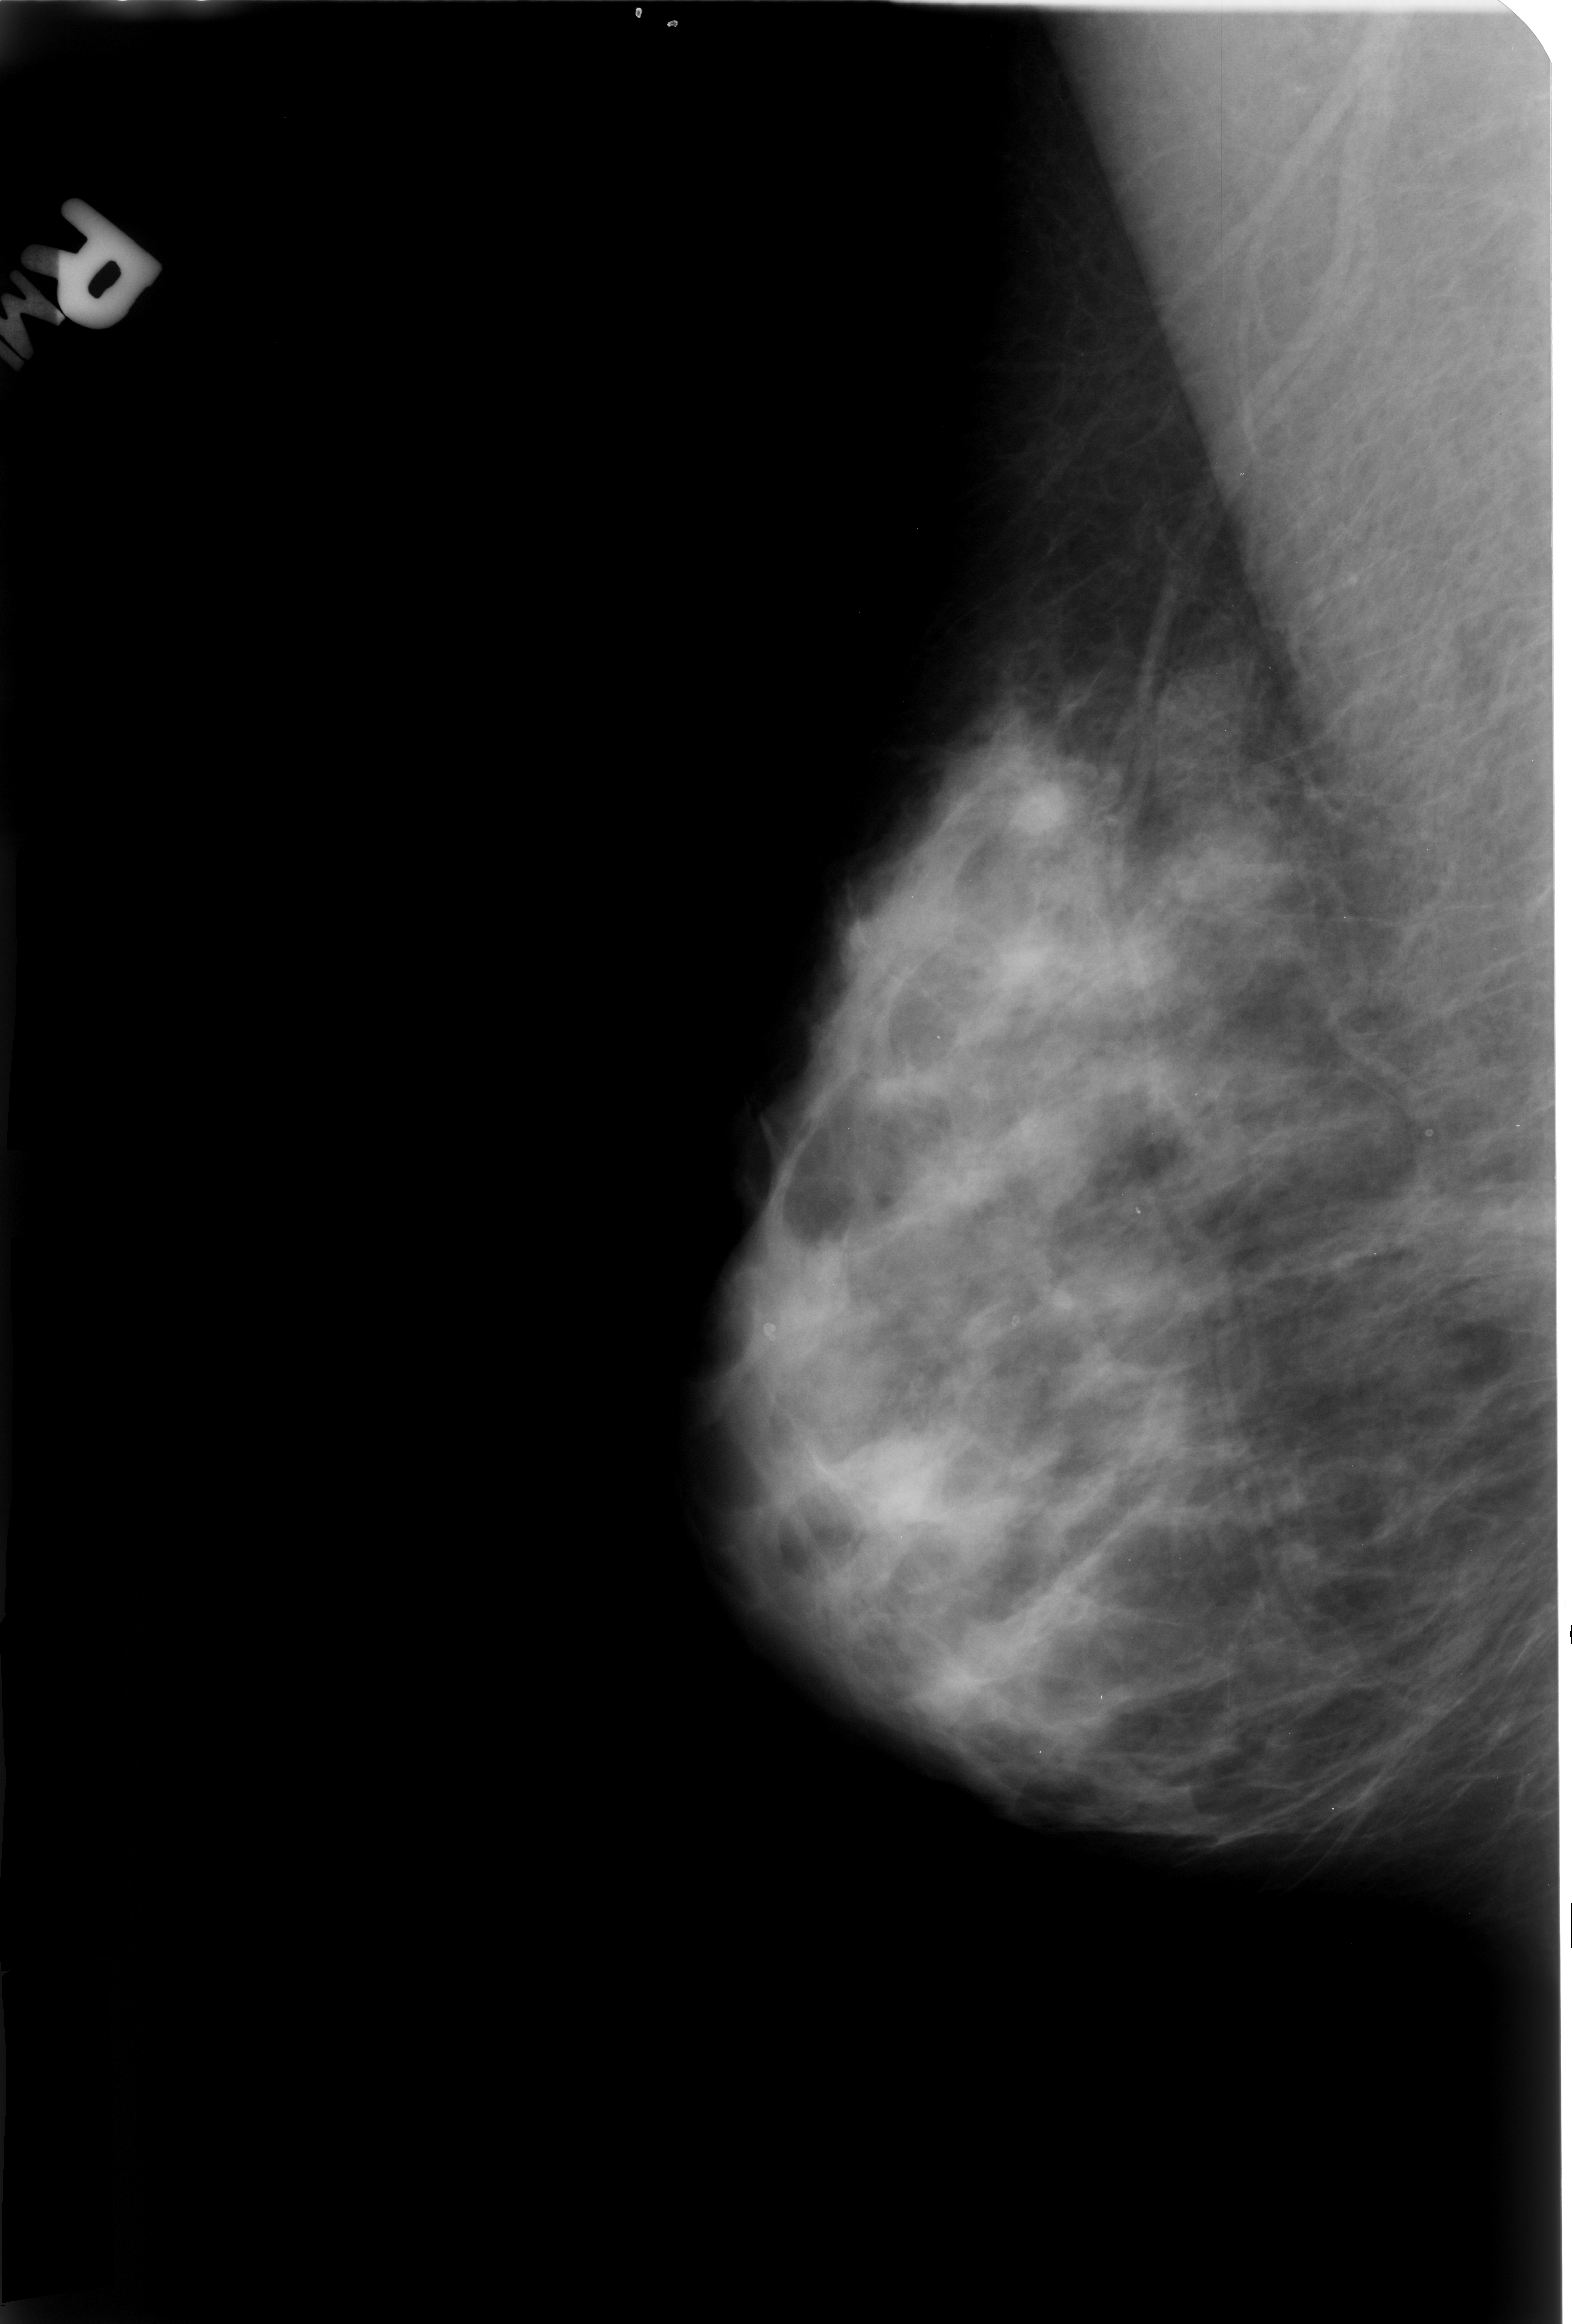
Scanned film-screen mammogram; right breast; MLO view; breast composition: heterogeneously dense (BI-RADS density category 3 of 4); 1572 × 2324 image matrix.
Expert-marked regions of interest on this film, with their recorded descriptors:
- calcifications, morphology lucent center; BI-RADS assessment category 2; subtlety rating 3 on a 1 (subtle) to 5 (obvious) scale; benign; no additional work-up was recommended (outcome (as recorded, no biopsy): benign without callback): bounding box <1119,1200,1157,1234> (left, top, right, bottom; pixels)